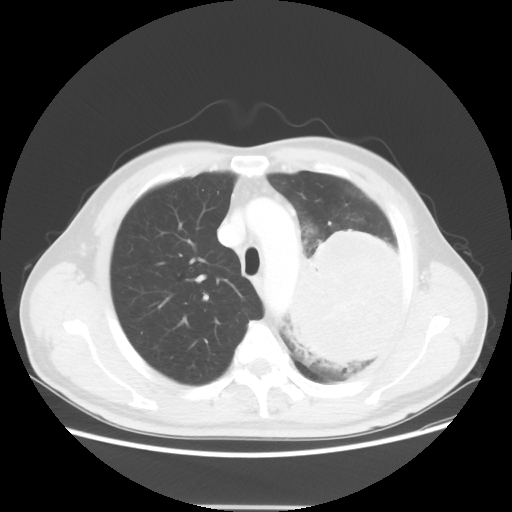
Chest CT, one axial slice; 100 kVp; lung window (W 1500 / L -600 HU); 5 mm slice thickness; 512 × 512 image matrix. Patient: male, 60 years. Case-level facts recorded for this patient, not image findings: clinical TNM (as recorded): T4 N1 M1a.
Structures marked on this image (rectangle marked by the reading radiologist):
- lung tumour (recorded histology: large cell carcinoma): bounding box [x1, y1, x2, y2] px = [282, 215, 410, 374]